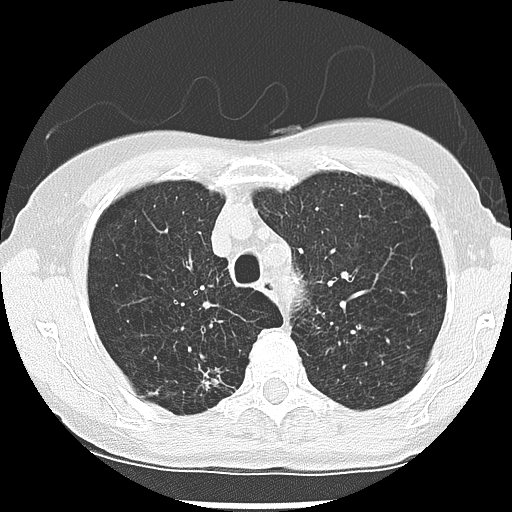
Low-dose screening chest CT, one axial slice. Slice 210 of 265 in the series (ordered by position). Lung window (W 1500 / L -600 HU). 512 × 512 image matrix, field of view 300 × 300 mm.
Structures marked on this image (outlined manually by an expert reader):
- lesion 1 (nodule, upper lobe of right lung): box from (x=203, y=373) to (x=219, y=388) px